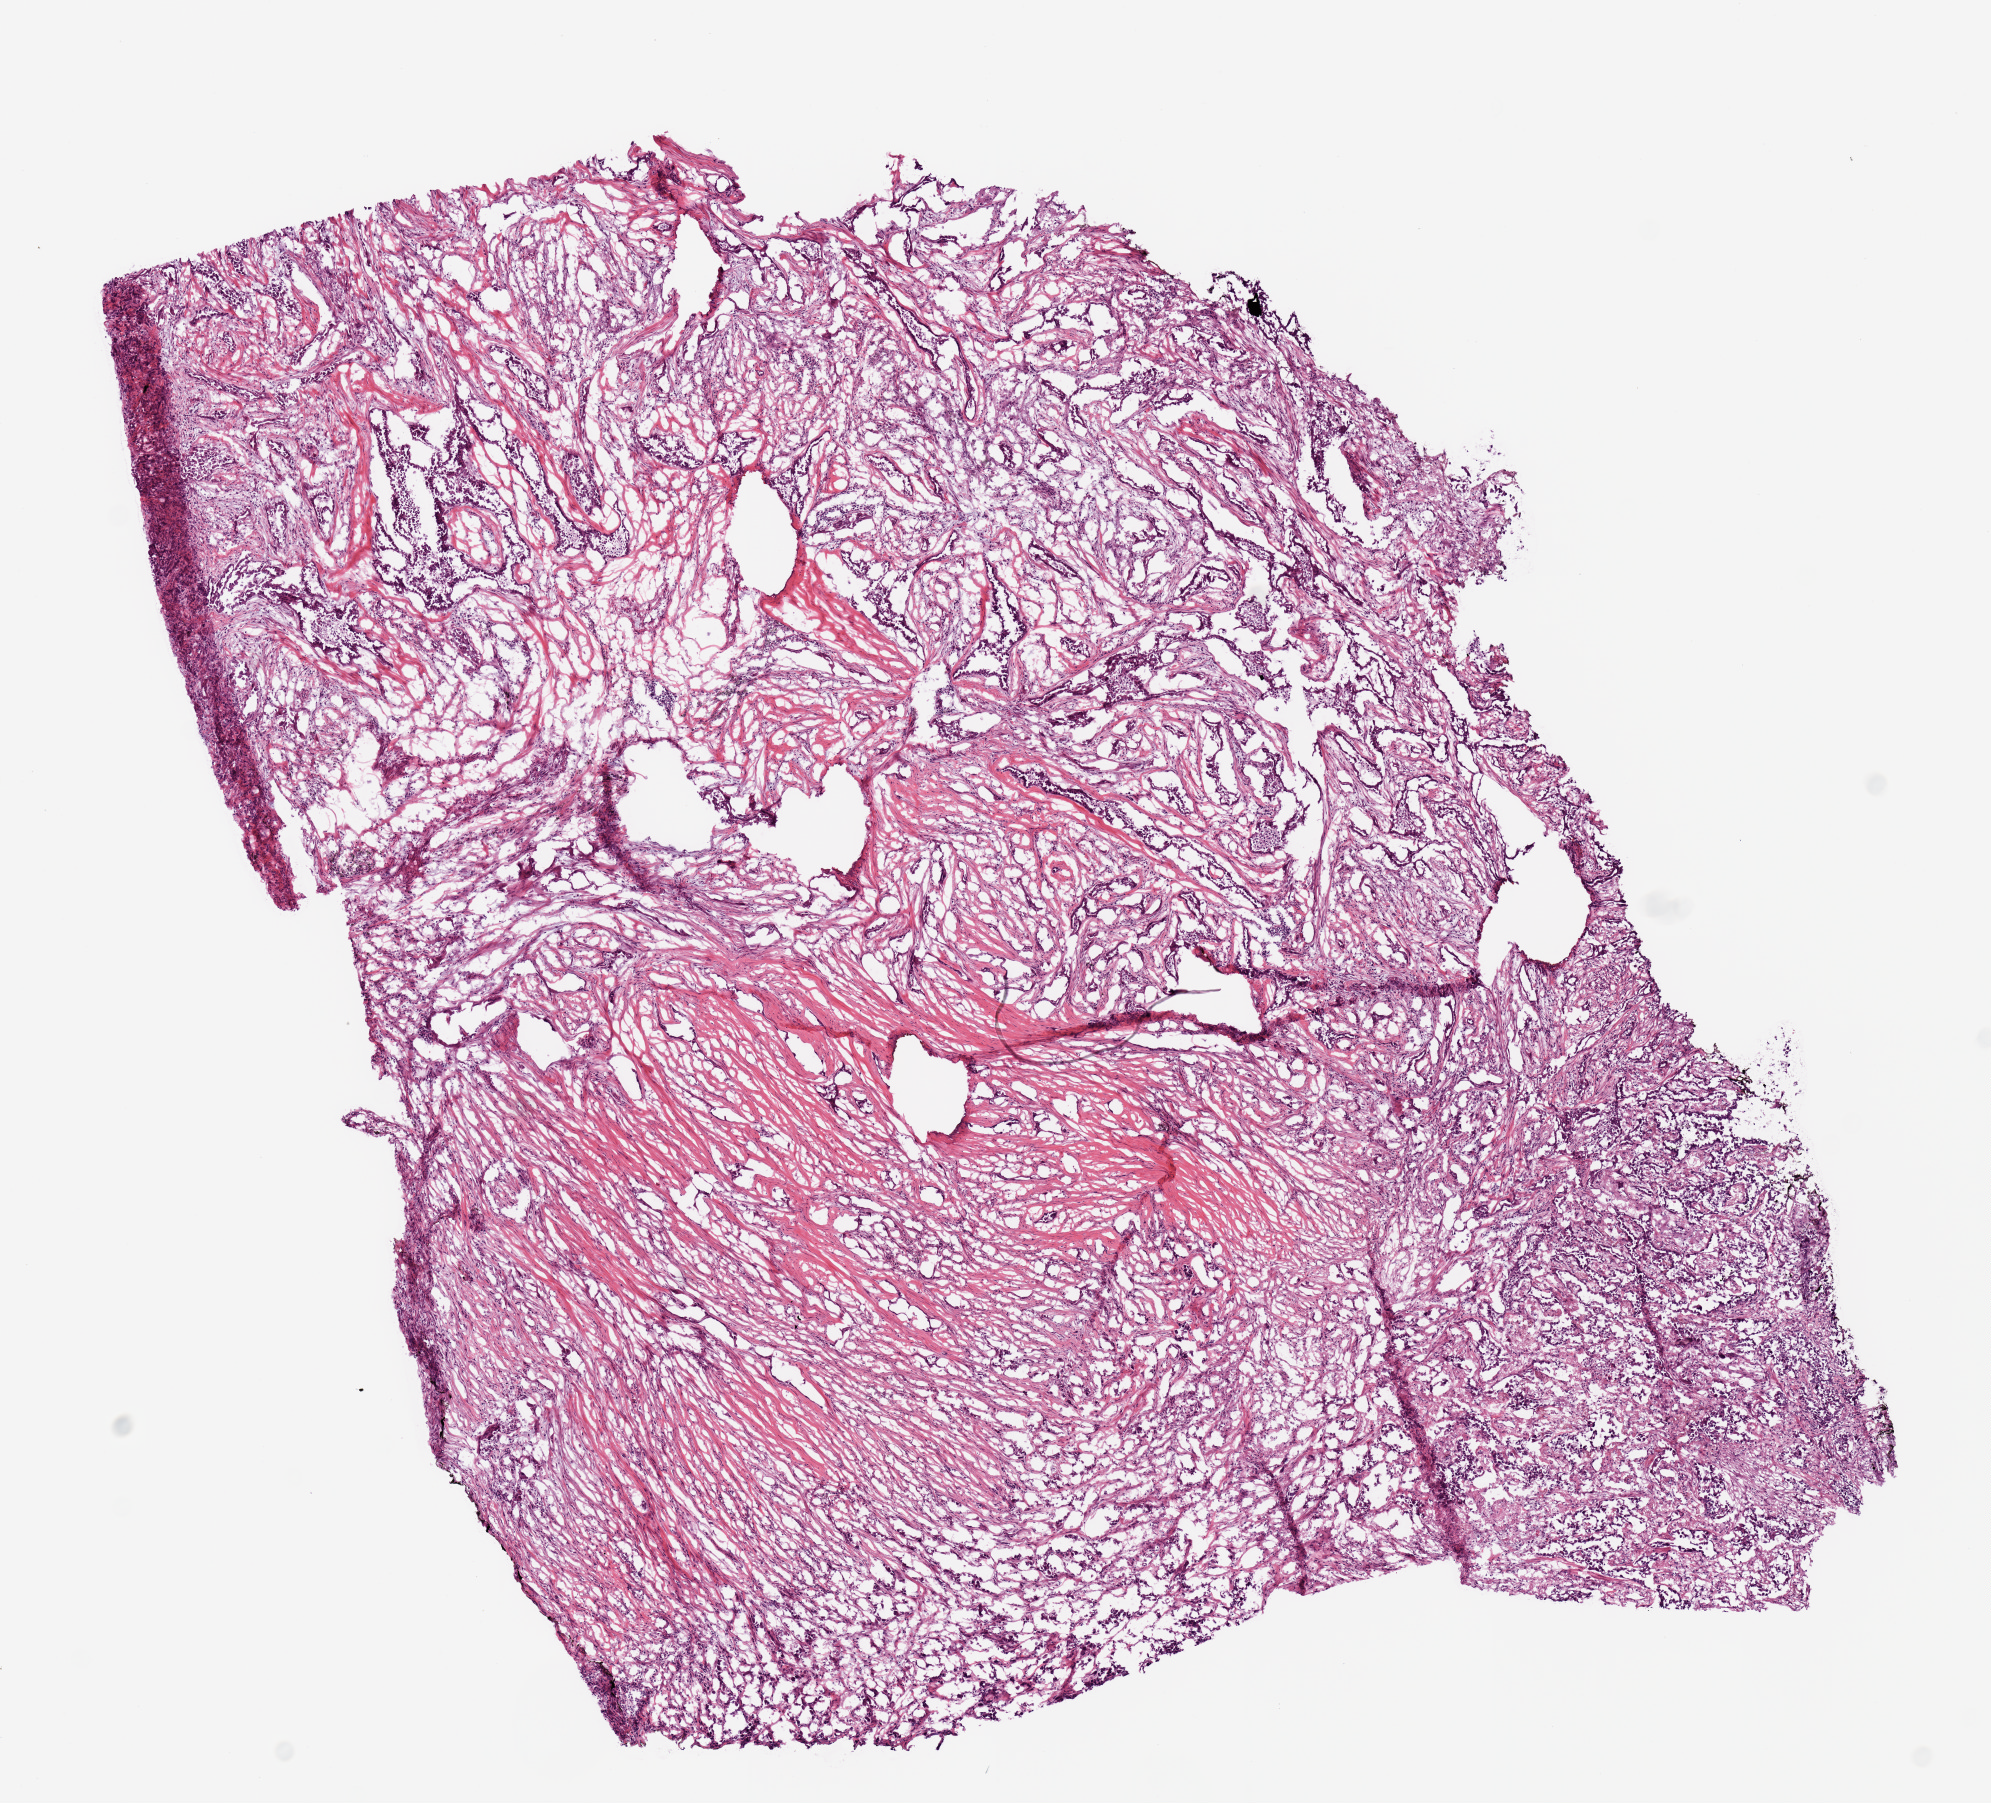
Hematoxylin and eosin (H&E) stained whole-slide image — shown as a low-resolution overview of the whole scanned area (about 7.9 x 7.1 mm), frozen section from the top of the tissue portion, lung, primary tumour sample. Female patient; age at initial diagnosis 70 years. Composition of this section per pathologist review: tumour cells 85%, tumour nuclei 65%, normal cells 0%, stromal cells 5%, necrosis 10%.
* AJCC pathologic stage: IA
* histologic diagnosis: Adenocarcinoma, NOS (middle lobe, lung)
* TNM: T1b N0 M0